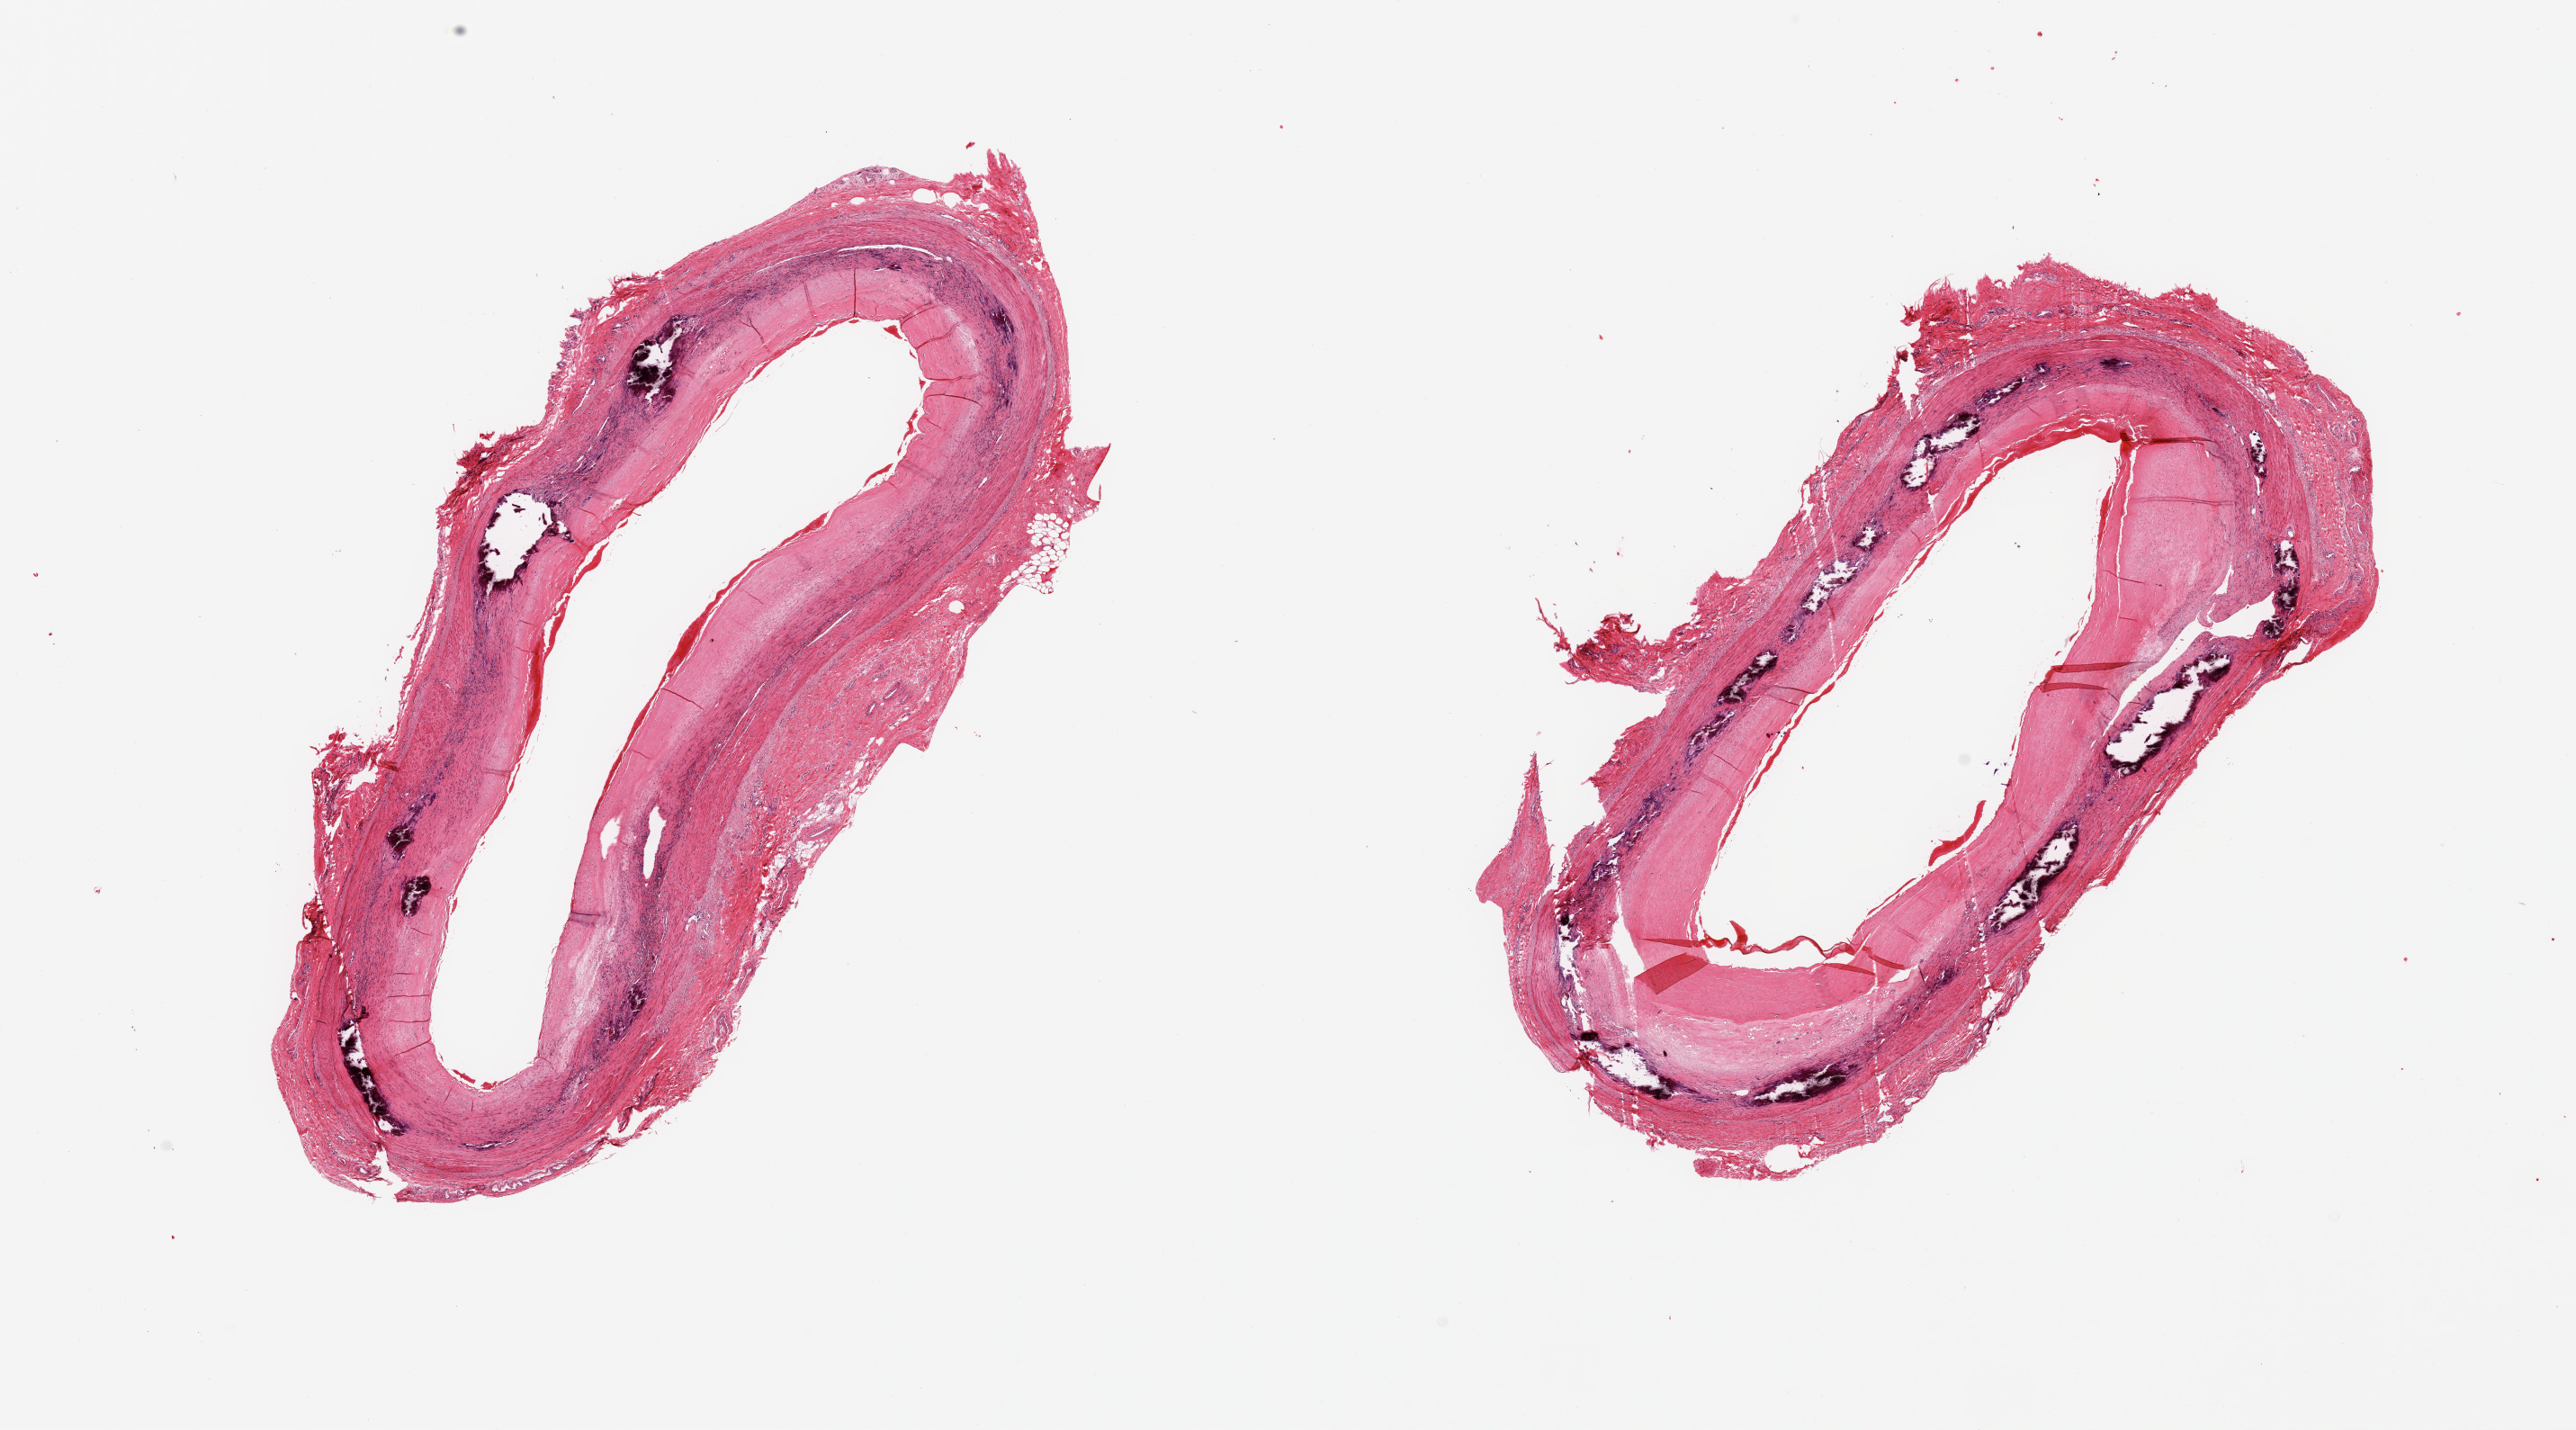
Whole-slide image, hematoxylin and eosin (H&E) stain, whole scanned area (about 22.6 x 12.6 mm, acquisition: 20x scan) shown as a low-resolution overview. PAXgene-fixed paraffin-embedded (PFPE) section. Target tissue: tibial artery. Tissue donor sample.
• review note (as recorded): 2 pieces; atherosclerosis, medial calcific sclerosis